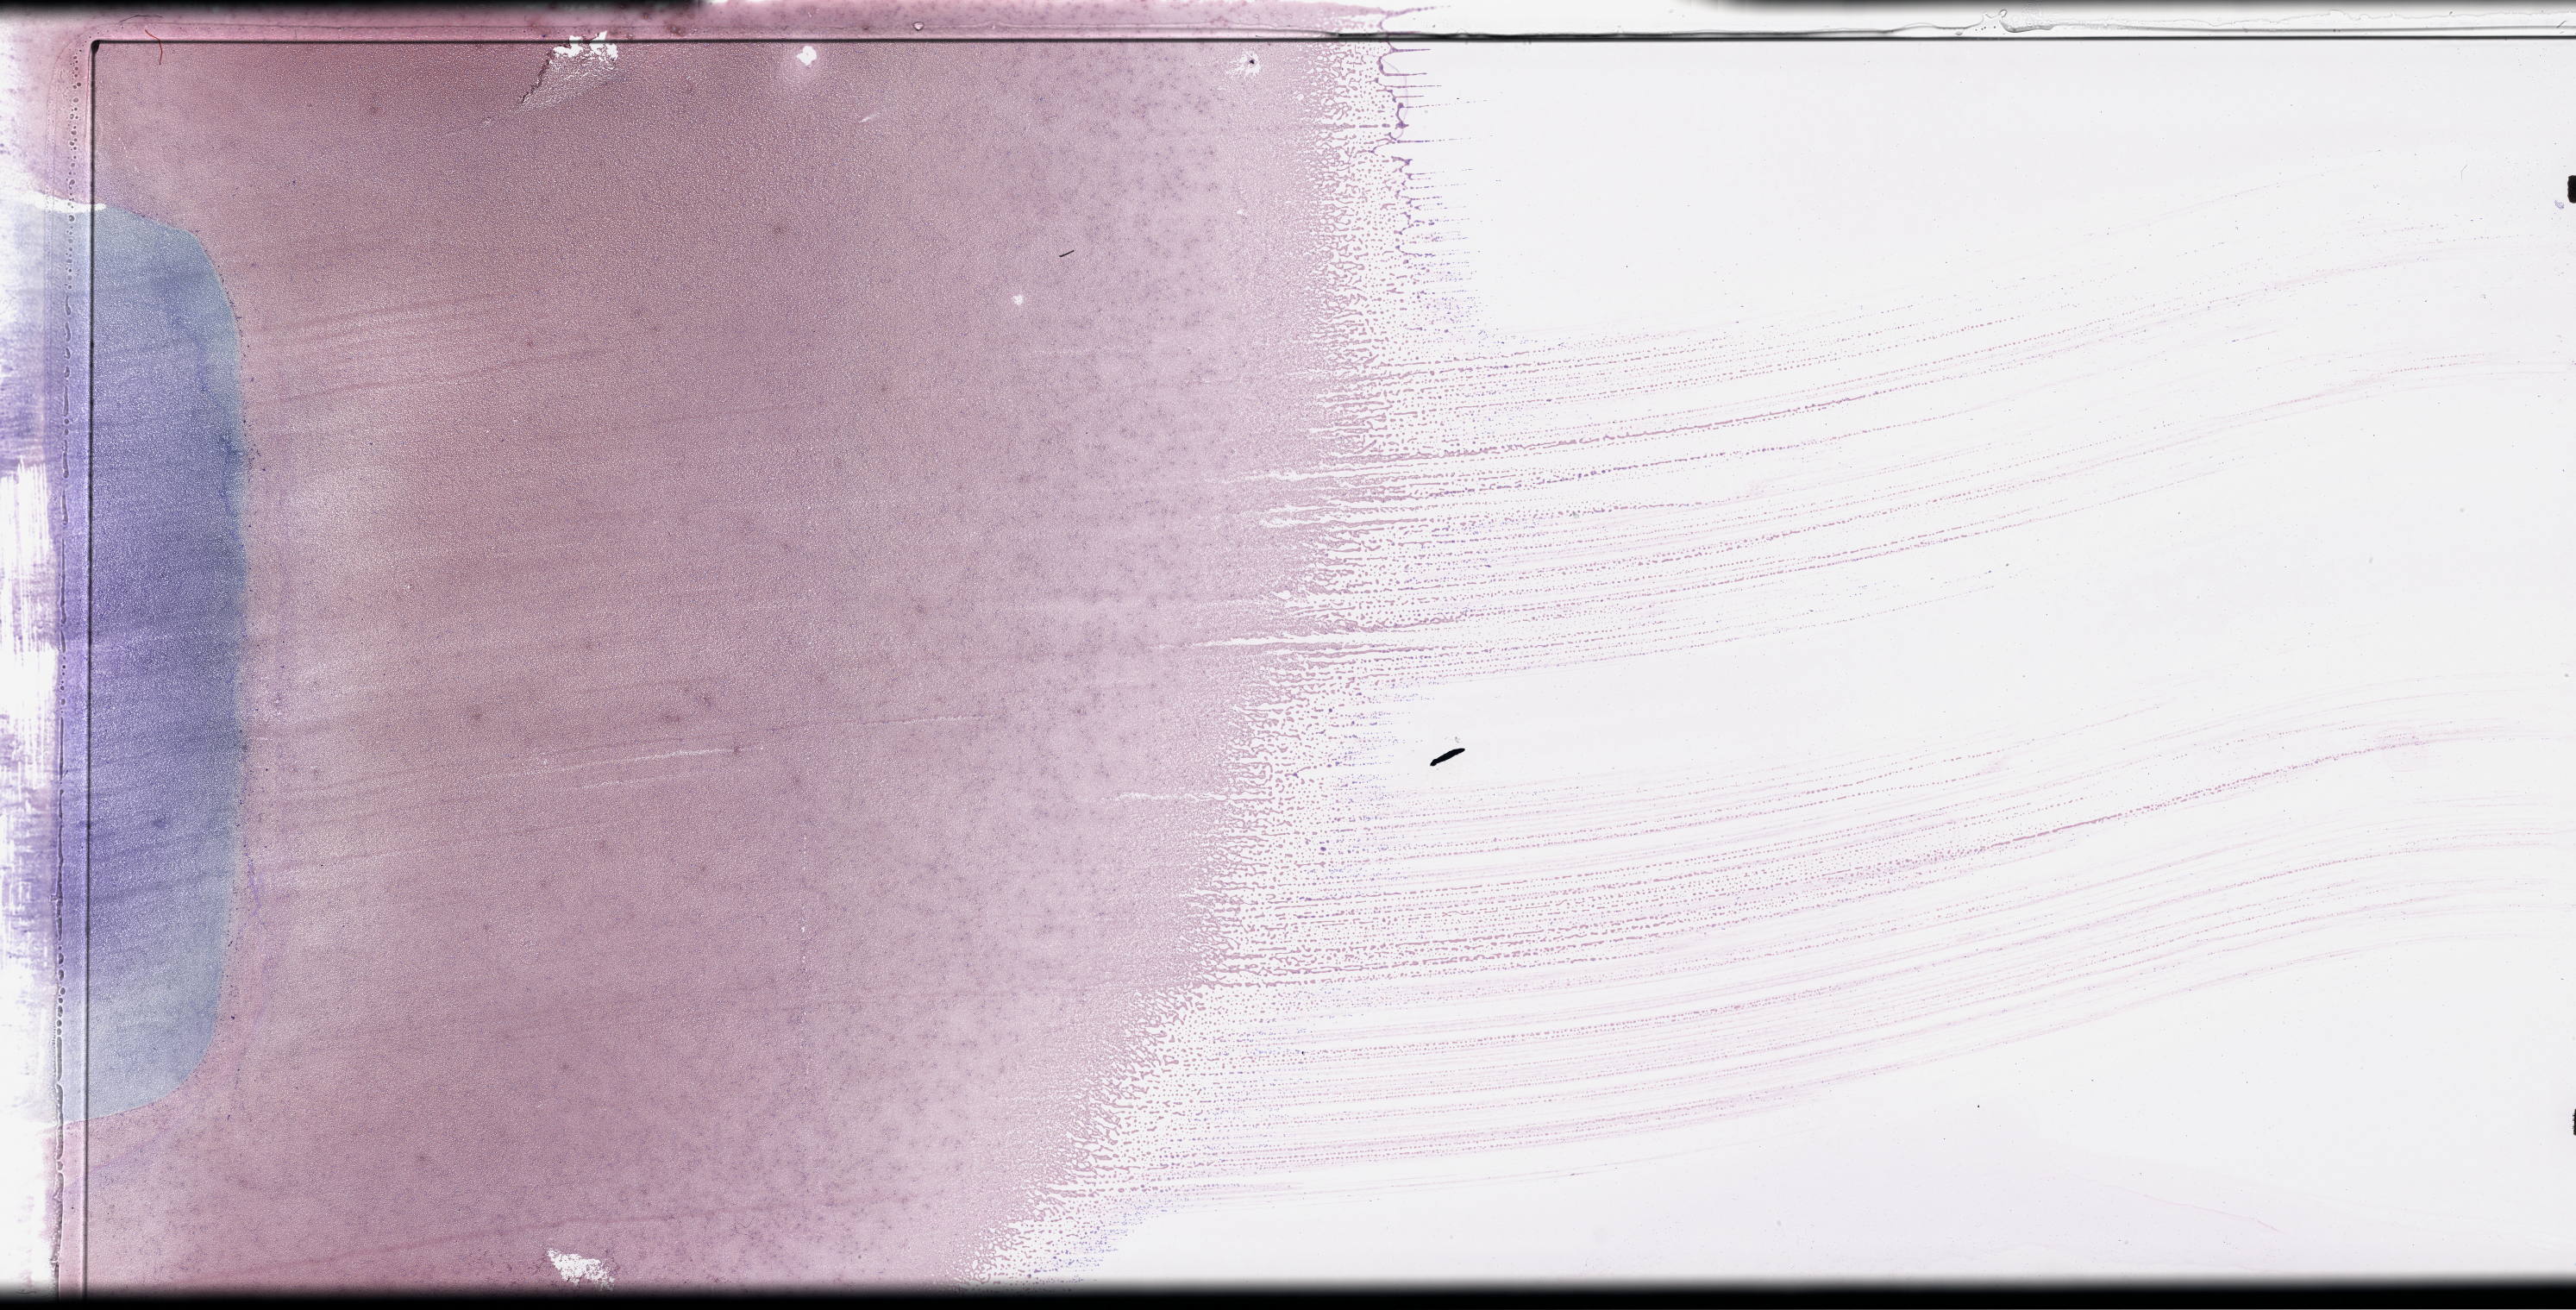
H&E whole-slide image — shown as a low-resolution overview of the whole scanned area (about 48.2 x 24.5 mm, from a 40x scan). Peripheral blood (leukaemic) sample. Patient: female, age 33 years.
FAB classification: M5. WHO classification: AML with t(9;11)(p22; q23); MLLT3-MLL. Diagnosis: Acute Myeloid Leukemia.